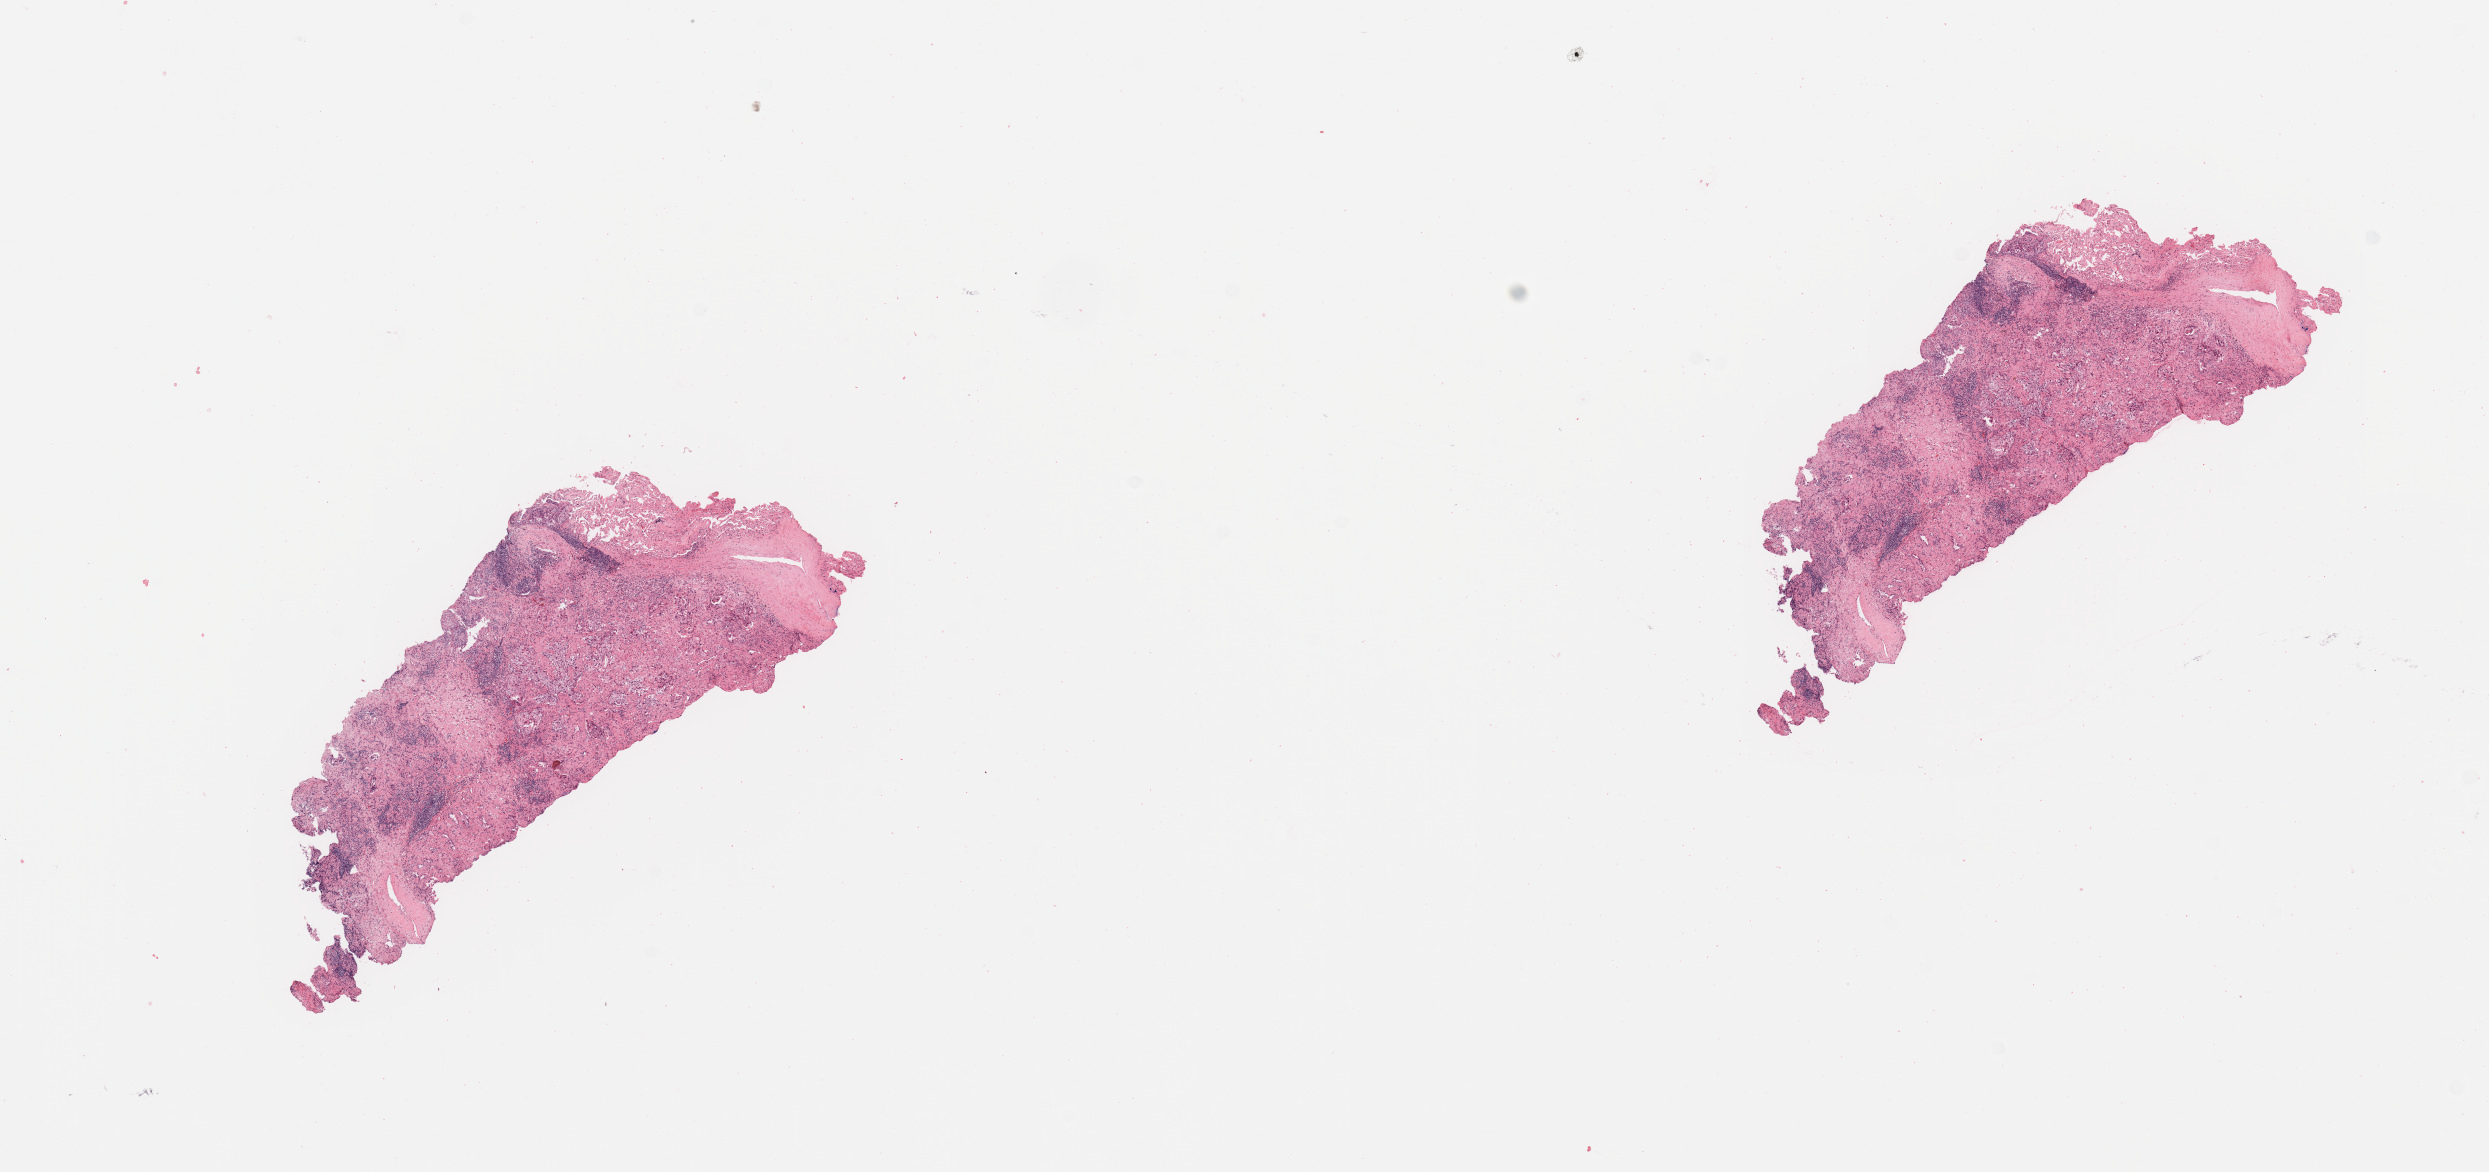
Hematoxylin and eosin (H&E) stained whole-slide image, a low-resolution overview of the entire scanned area, about 19.7 x 9.3 mm (from a 20x scan). Lung, tissue type not recorded.
Patient diagnosis (cohort enrolment): lung adenocarcinoma (lung).